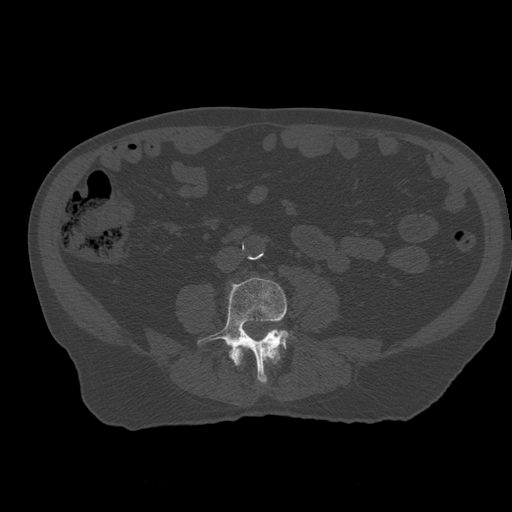
CT including the spine, one axial slice; slice 167 of 399 in the series (ordered by position); 120 kVp; bone window (W 1800 / L 400 HU); 1.25 mm slice thickness; 512 × 512 image matrix, field of view 407 × 407 mm. Patient age 73 years. Case-level facts recorded for this patient, not image findings: primary cancer: prostate; vertebrae with lytic lesions (as recorded): L2.
Structures marked on this image (semi-automatic segmentation, software-assisted and operator-edited):
- L3 vertebra: bounding box (x1, y1, x2, y2) in pixels: (235, 342, 280, 364)
- L4 vertebra: (198, 278, 294, 383)